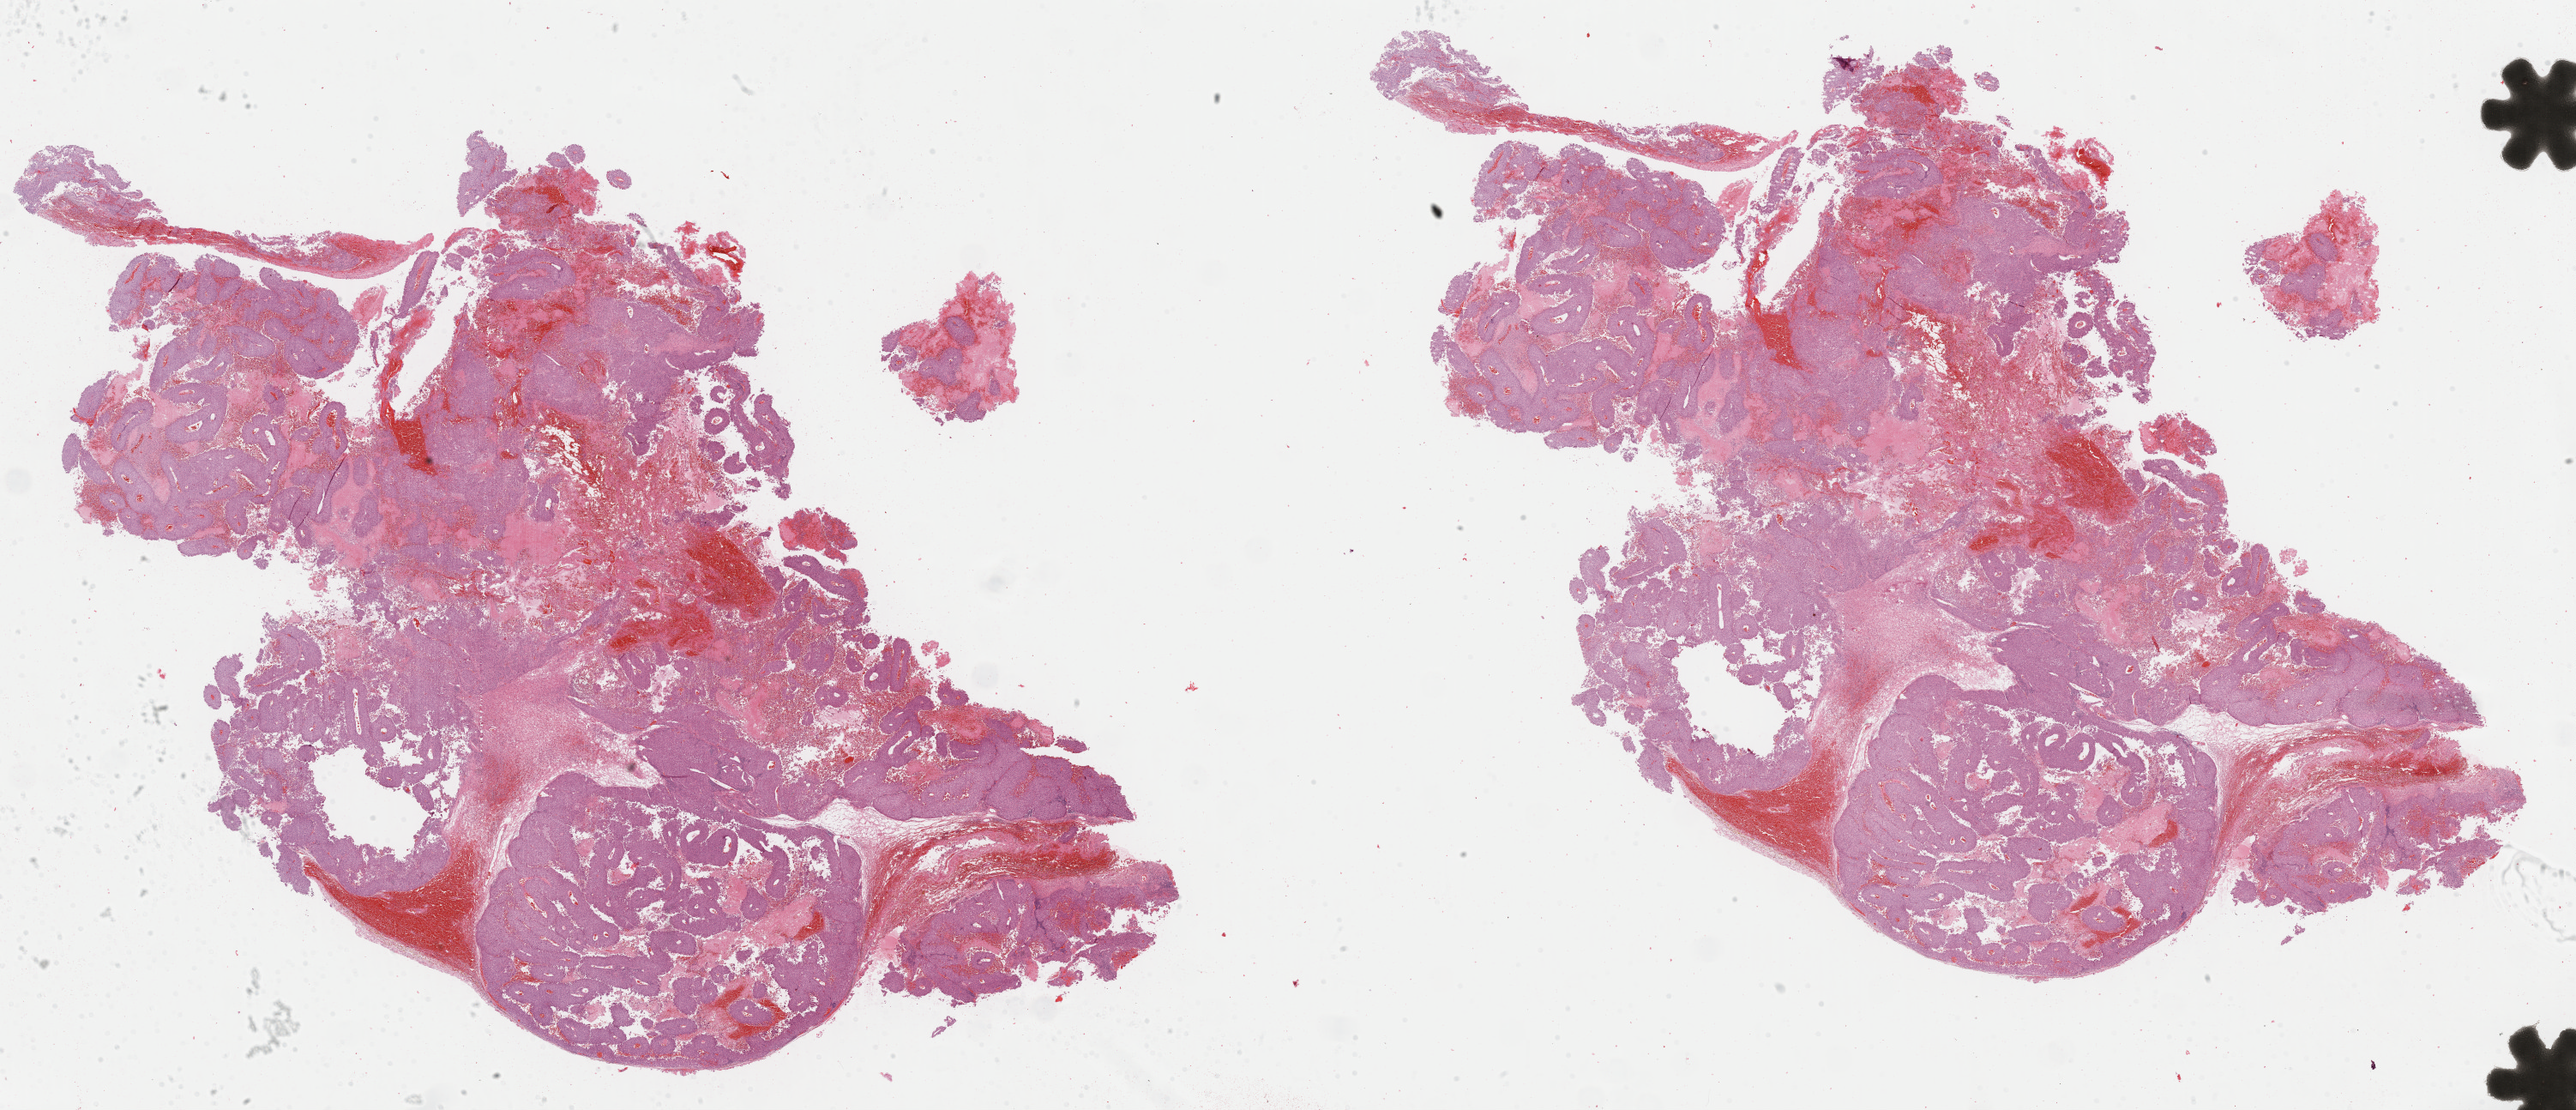
H&E whole-slide image — low-resolution overview of the scanned area, about 47.4 x 20.4 mm, formalin-fixed paraffin-embedded (FFPE) diagnostic section, metastatic tumour sample. Patient: male, age at initial diagnosis 30 years.
• this section: metastatic tumour tissue
• patient diagnosis: Malignant melanoma, NOS